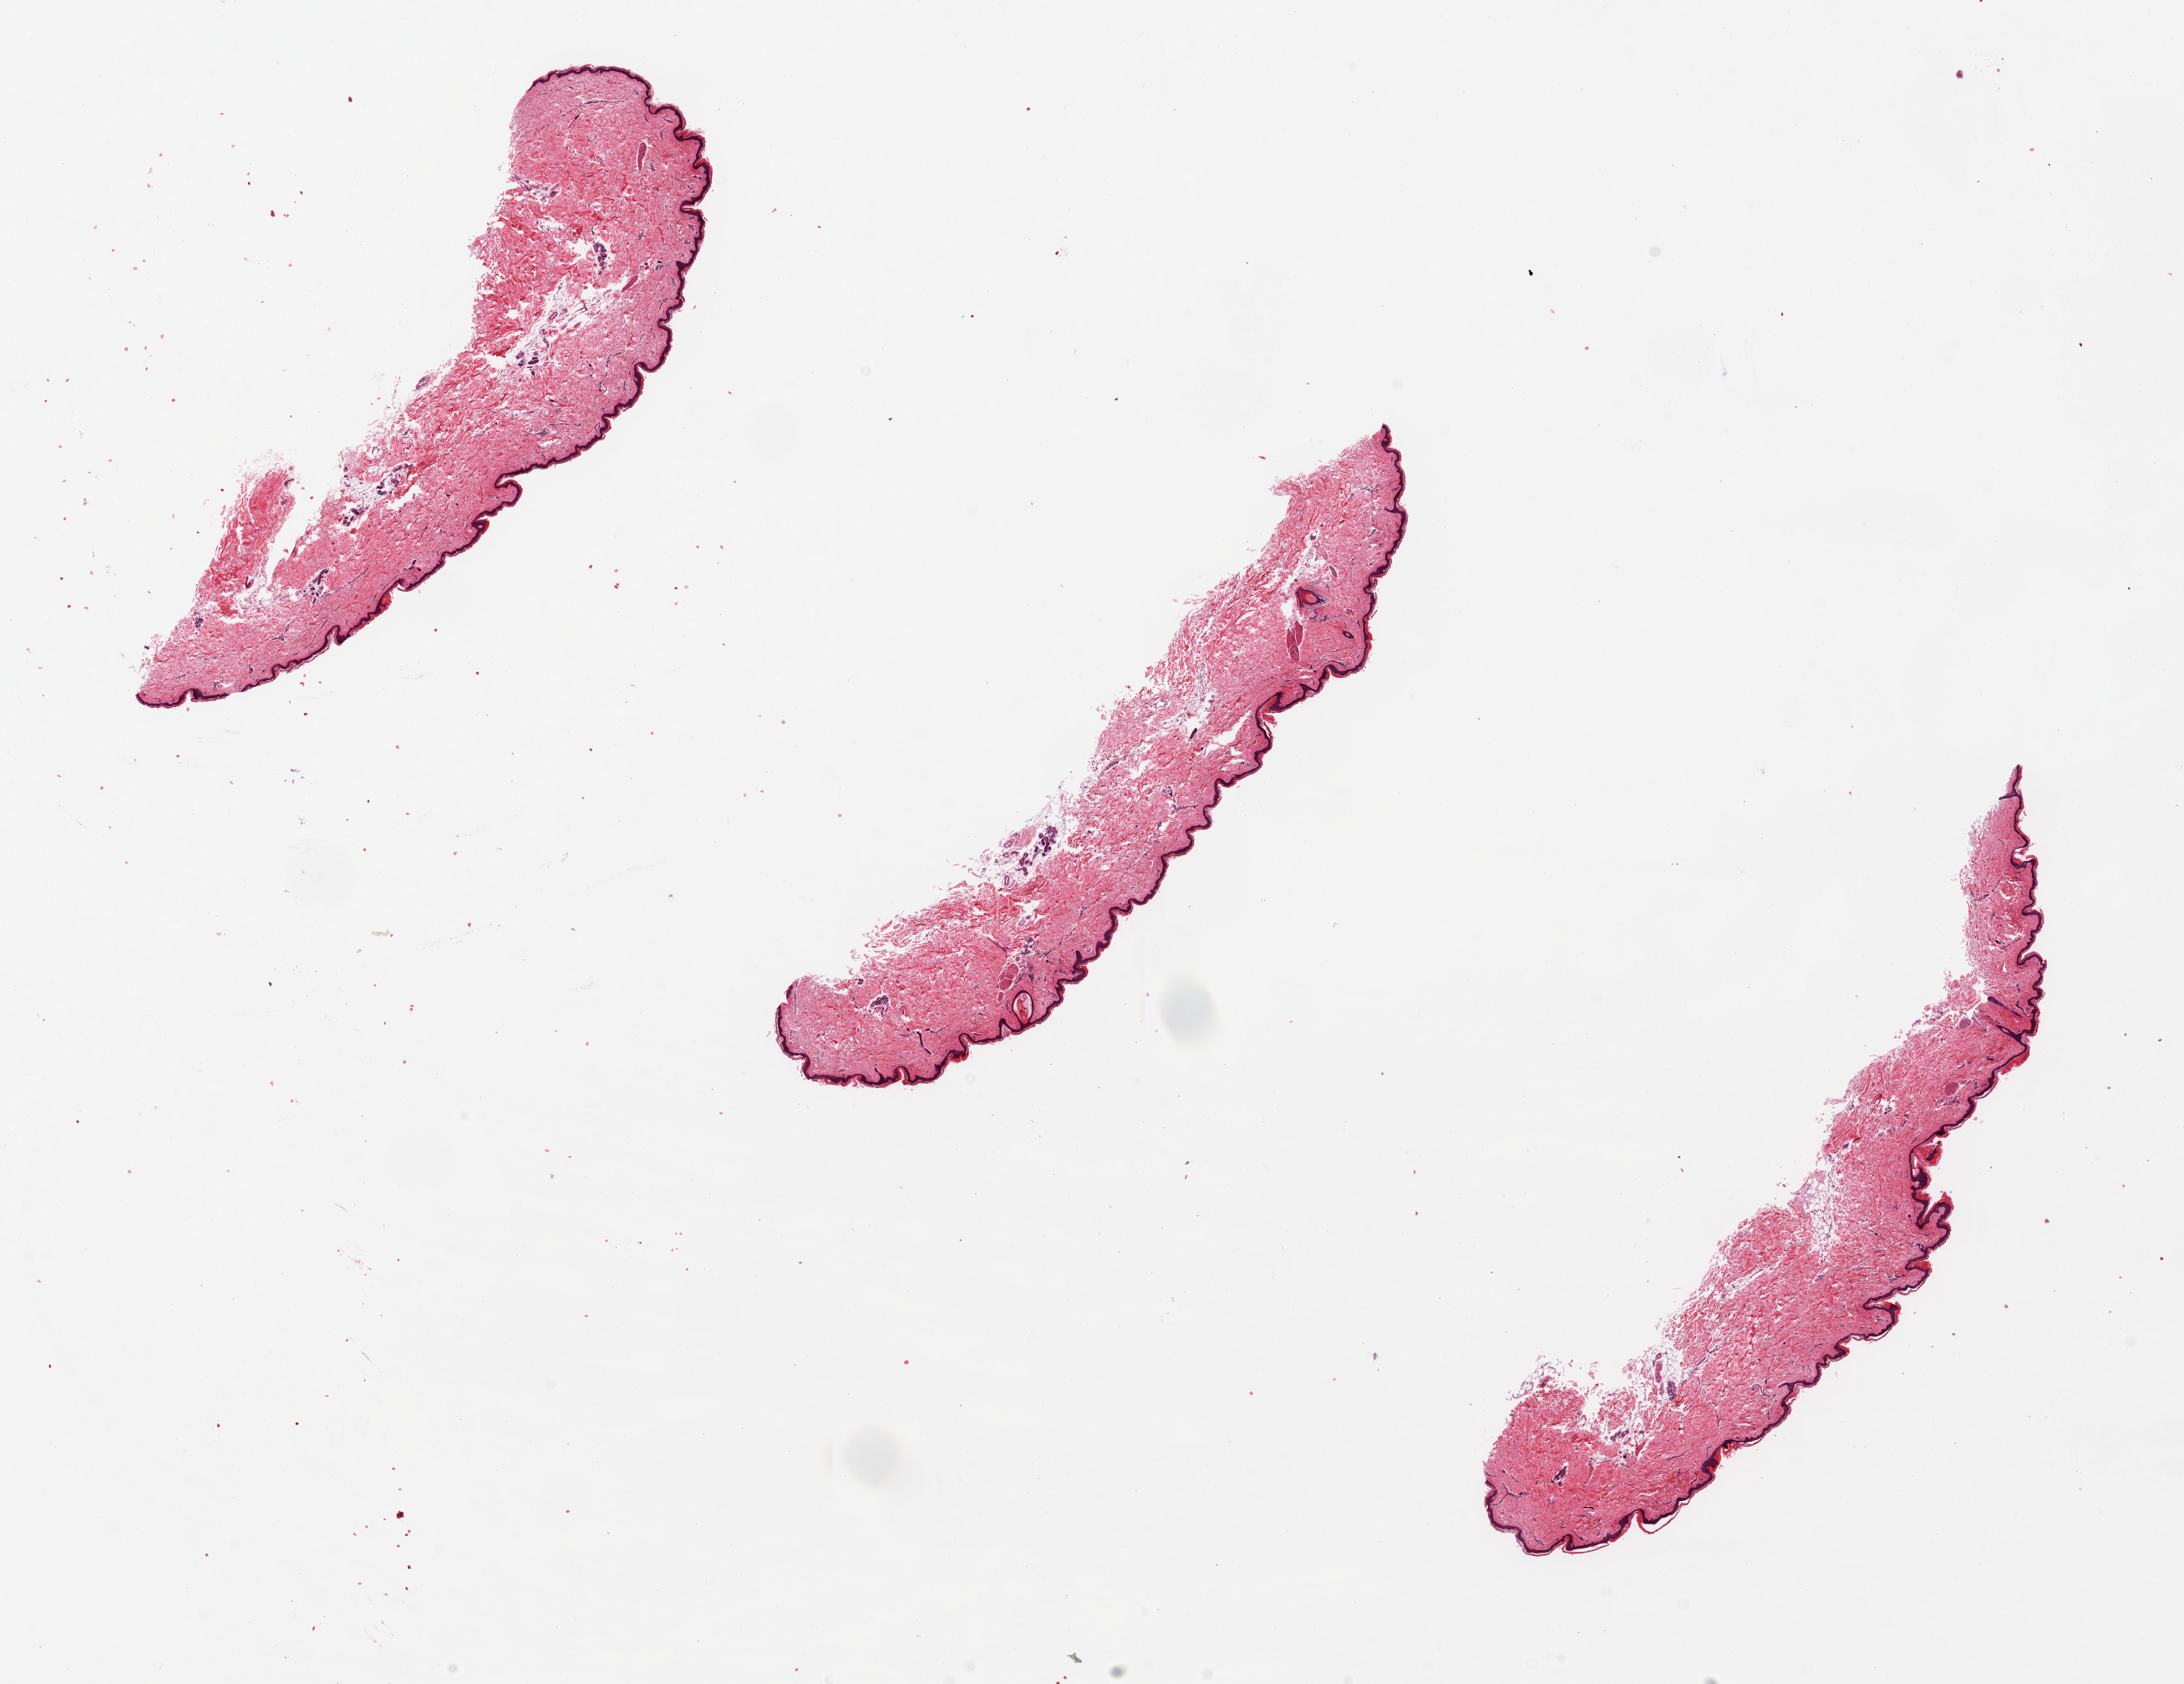
H&E whole-slide image, brightfield, whole scanned area (about 20.7 x 15.9 mm) shown as a low-resolution overview; PAXgene-fixed, paraffin-embedded tissue; target tissue: skin of lower leg; tissue donor sample. Donor: female.
Review note (as recorded): 3 ~8x1.5mm pieces. Squamous epithelium is 1-2% of thickness.